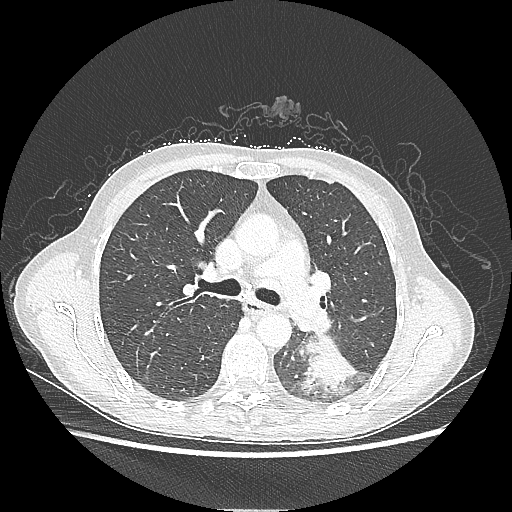
Chest CT, one axial slice; position 137 of 220 along the scan axis; reconstruction kernel LUNG; 80 kVp; lung window (W 1500 / L -600 HU); 512 × 512 image matrix, field of view 360 × 360 mm. Patient: female, 53 years. From the clinical record (not read from this slice): clinical TNM (as recorded): T3 N0 M0.
Outlined on this slice (rectangle marked by the reading radiologist):
- lung tumour (recorded histology: adenocarcinoma): bounding box <298,338,358,397> (left, top, right, bottom; pixels)